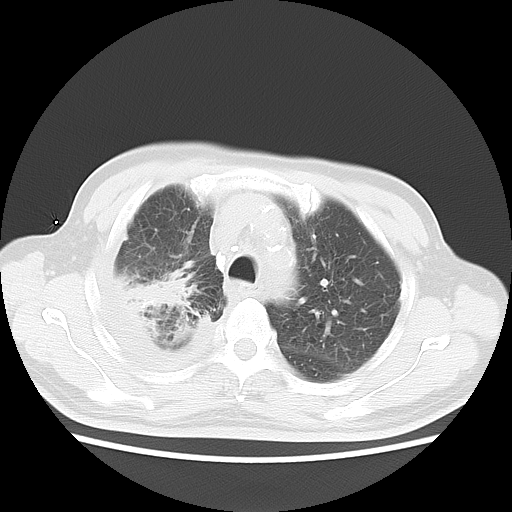
Chest CT, one axial slice; position 12 of 20 along the scan axis; lung window (W 1500 / L -600 HU); 5 mm slice thickness; 512 × 512 image matrix. Male patient, age 75 years. Case-level facts recorded for this patient, not image findings: clinical TNM (as recorded): T1c N1 M1.
Annotated regions visible in this slice (bounding box drawn by a radiologist):
- lung tumour (recorded histology: adenocarcinoma): bounding box (x1, y1, x2, y2) in pixels: (117, 268, 204, 315)